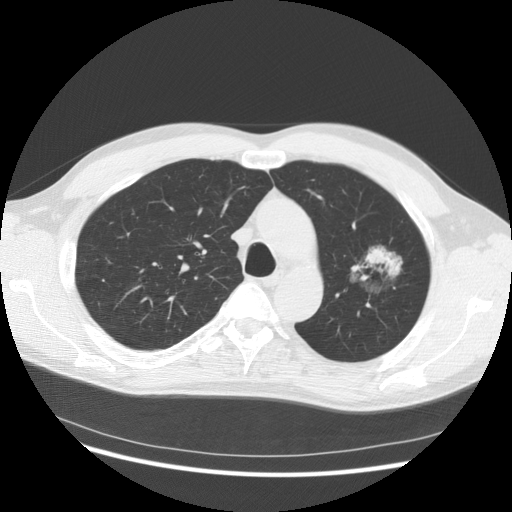
Low-dose screening chest CT, one axial slice; lung window (W 1500 / L -600 HU); 512 × 512 image matrix.
Outlined on this slice (manually delineated by an expert):
- lesion 1 (tumor, upper lobe of left lung): bounding box [x1, y1, x2, y2] px = [366, 248, 401, 275]